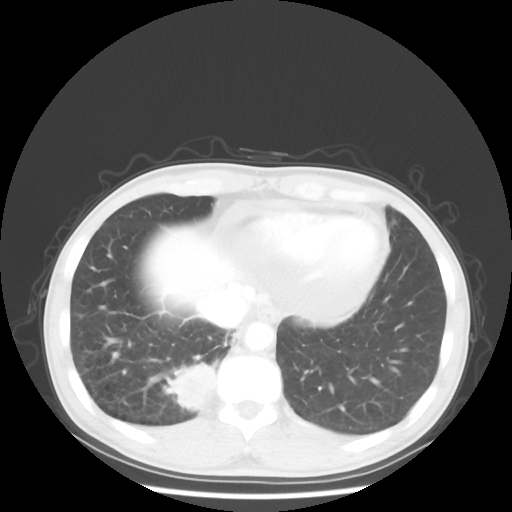
Chest CT, one axial slice. Position 11 of 58 along the scan axis. Lung window (W 1500 / L -600 HU). 5 mm slice thickness. 512 × 512 image matrix, field of view 360 × 360 mm. Patient: male, 56 years. Case-level facts recorded for this patient, not image findings: clinical TNM (as recorded): T2 N1 M1.
Structures marked on this image (rectangle marked by the reading radiologist):
- lung tumour (recorded histology: adenocarcinoma): bounding box [x1, y1, x2, y2] px = [166, 359, 214, 413]